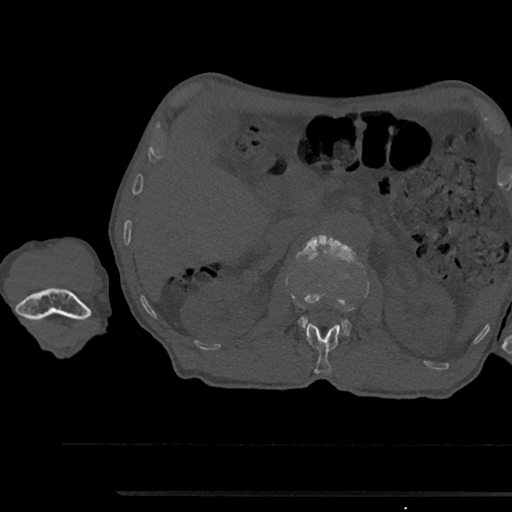
CT including the spine, one axial slice. Slice 609 of 797 in the series (ordered by position). 120 kVp. Bone window (W 1800 / L 400 HU). 0.5 mm slice thickness. 512 × 512 image matrix, field of view 367 × 367 mm. Patient: male, 79 years. Case-level facts recorded for this patient, not image findings: primary cancer: prostate.
Outlined on this slice (semi-automatic segmentation, software-assisted and operator-edited):
- L1 vertebra: bounding box (x1, y1, x2, y2) in pixels: (306, 323, 340, 374)
- L2 vertebra: (296, 234, 357, 336)